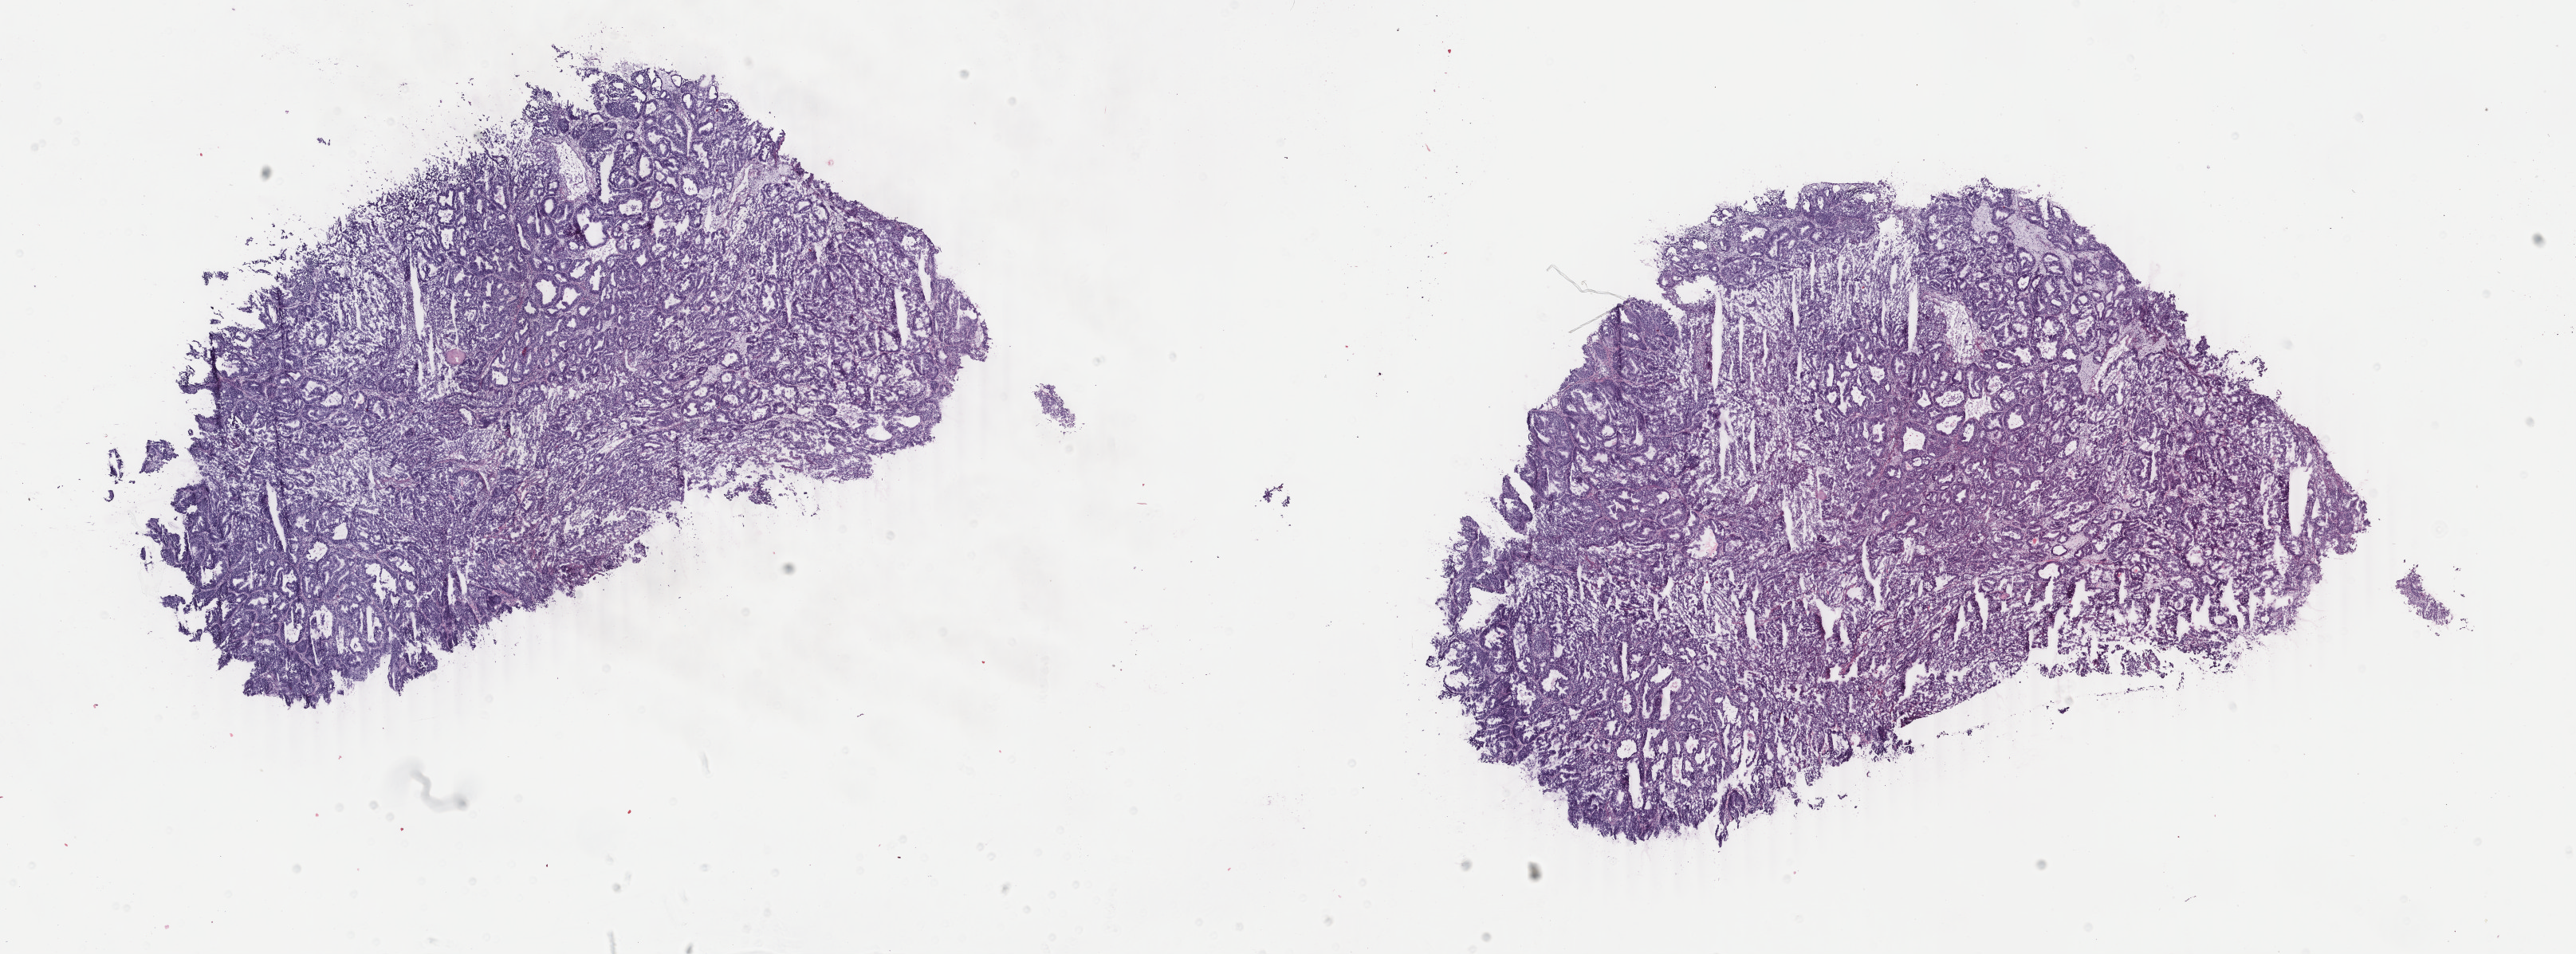
H&E-stained whole-slide image, shown as a low-resolution overview of the whole scanned area (about 25.7 x 9.5 mm), frozen section, uterus, primary tumour sample. Female, age 58 years at initial diagnosis. Histologic grade: G1 (well differentiated). Pathologist review of this section (percent, as recorded): tumour cells 82%, tumour nuclei 90%, normal cells 0%, stromal cells 8%, necrosis 10%. Infiltration values recorded for this section: lymphocyte infiltration 4%, monocyte infiltration 3%, neutrophil infiltration 1%.
* diagnosis: Endometrioid adenocarcinoma, NOS (endometrium)
* FIGO stage: IA